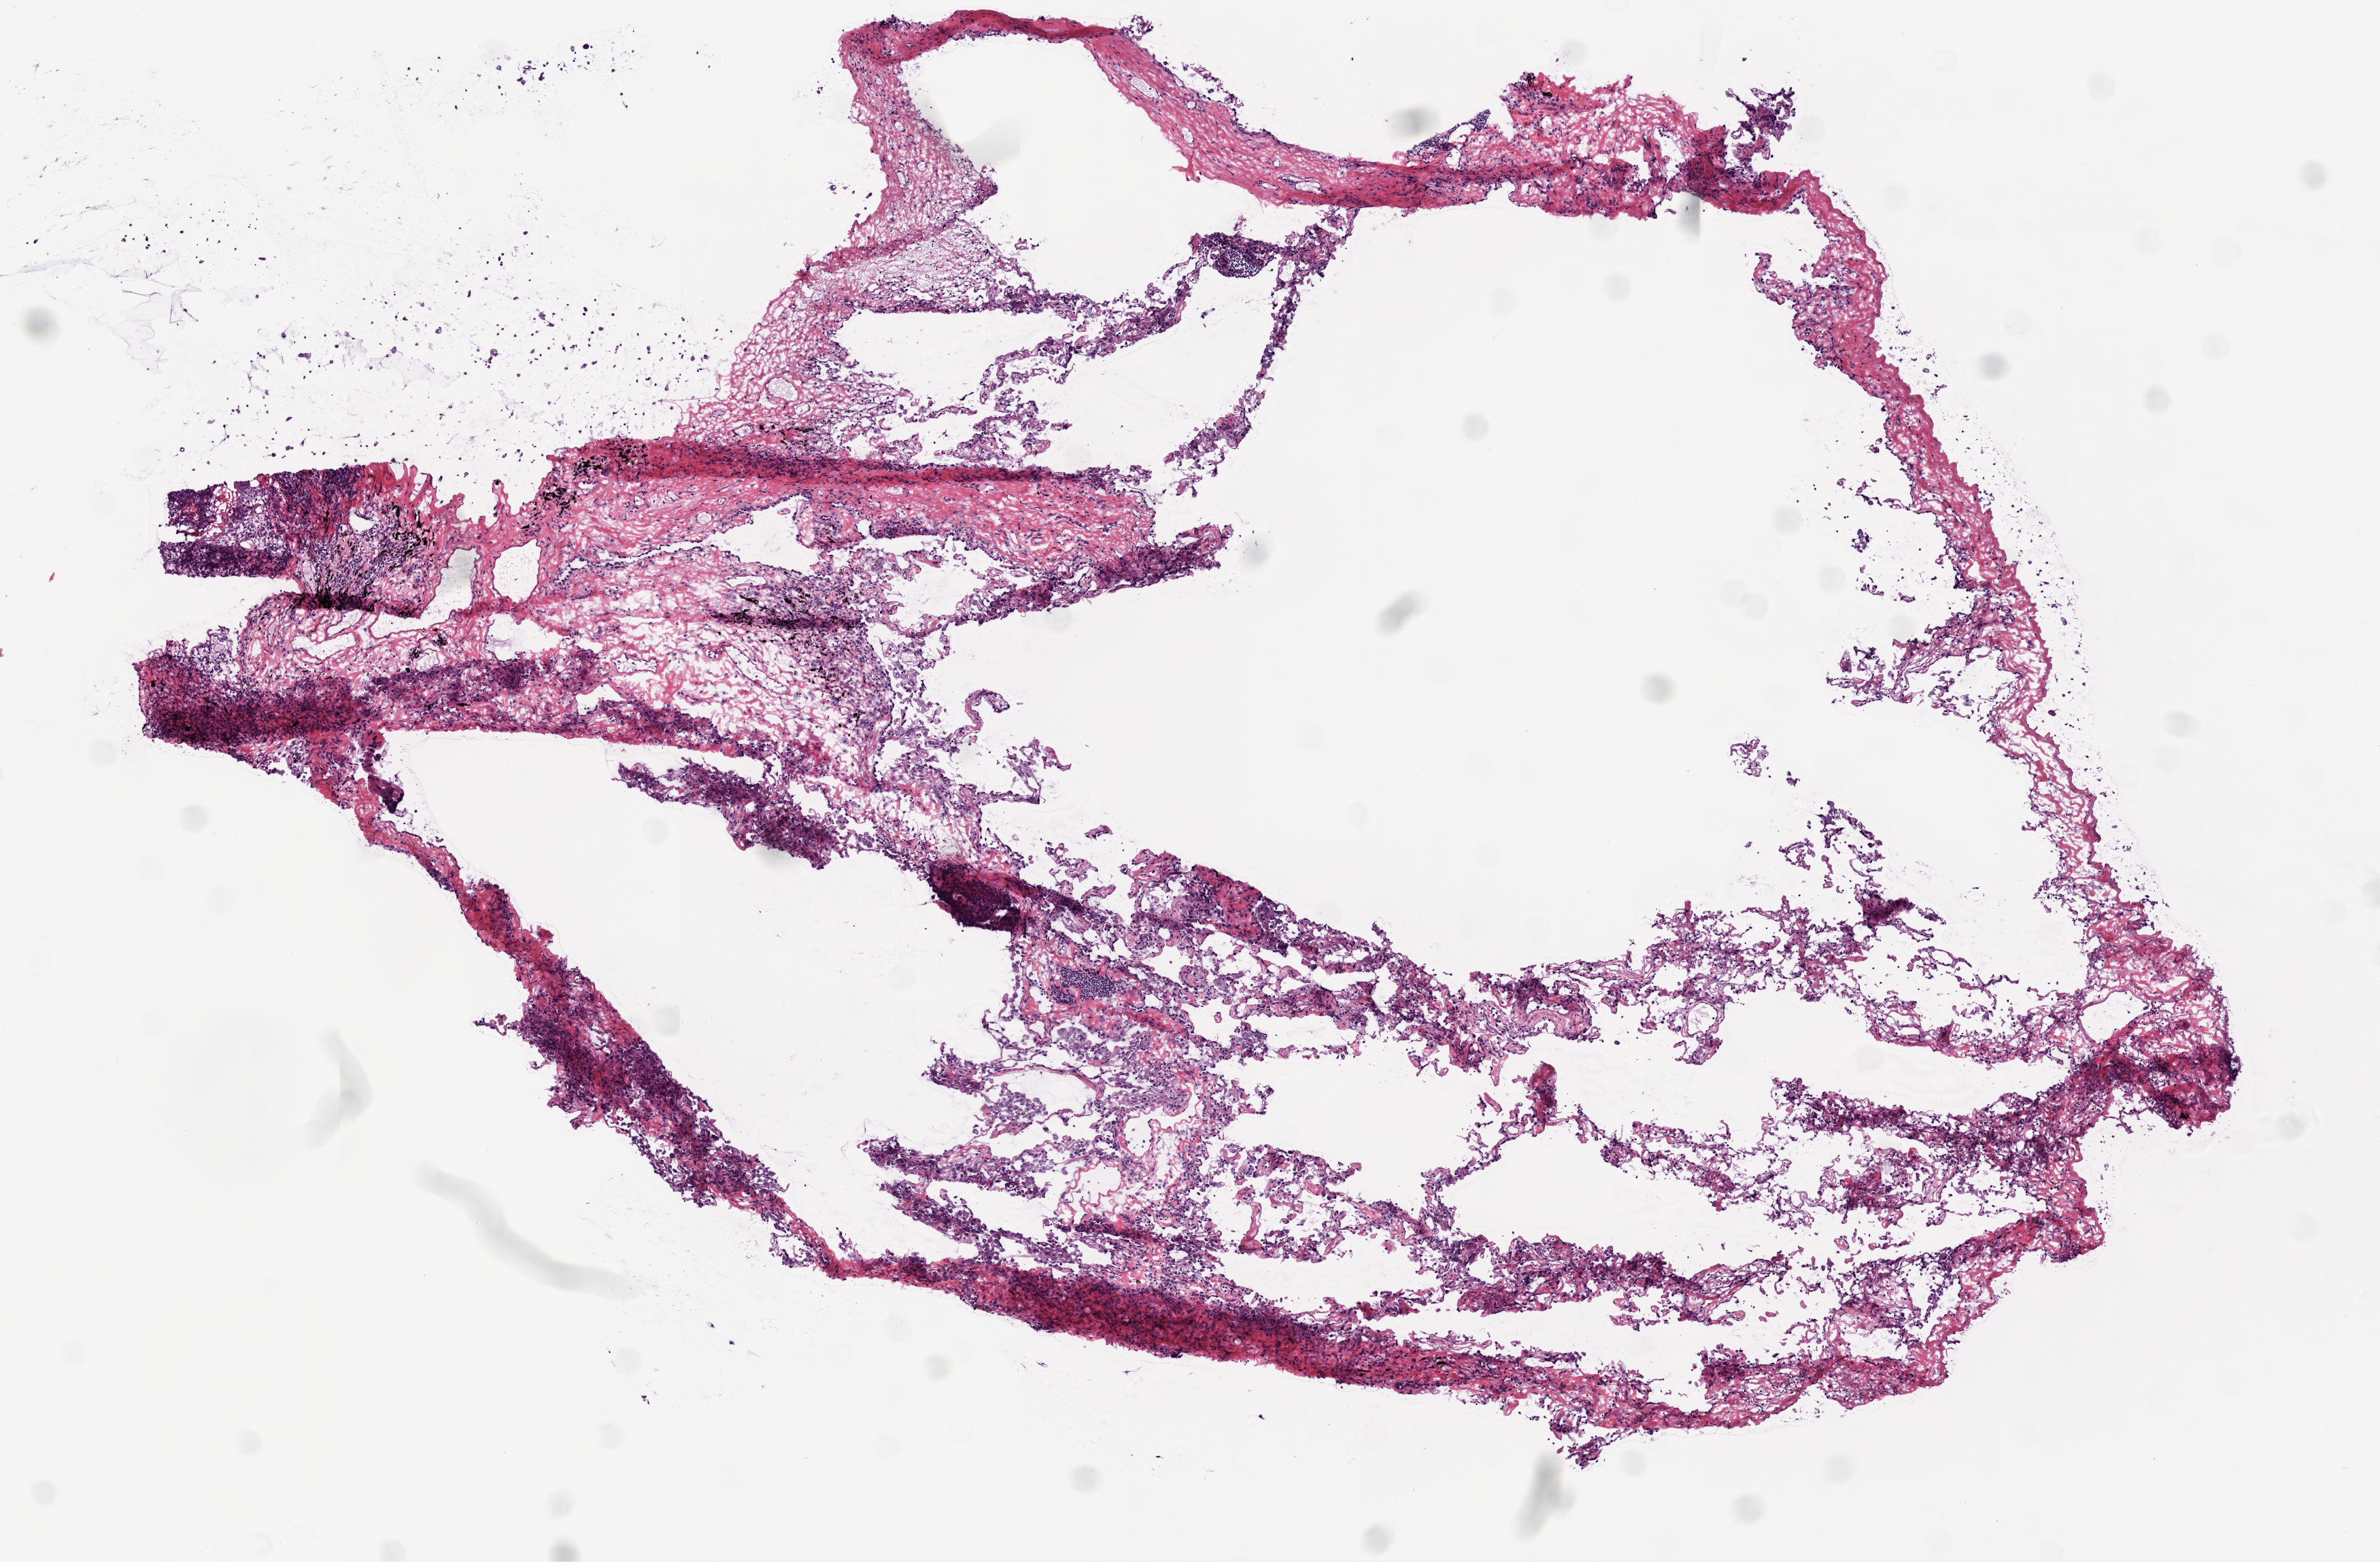
H&E whole-slide image — shown as a low-resolution overview of the whole scanned area (about 7.0 x 4.6 mm). Frozen section from the top of the tissue portion. Lung, solid tissue normal (non-tumour tissue) sample. Male, age 60 years at initial diagnosis.
This section: solid tissue normal (non-tumour) sample from the same patient. Patient diagnosis: Squamous cell carcinoma, NOS (upper lobe, lung).